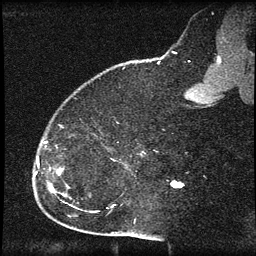
Breast MRI (dynamic contrast-enhanced), one sagittal slice. Position 17 of 60 along the scan axis. Dynamic contrast-enhanced series, image 2 of 3 at this slice position (ordered by acquisition). 1.5 T. TE 4.2 ms, TR 8.2 ms. 256 × 256 image matrix, field of view 180 × 180 mm. Patient: female, 32 years.
Annotated regions visible in this slice (semi-automatic segmentation, software-assisted and operator-edited):
- analysis volume of interest (the breast-tissue region the enhancement analysis was run in; not a lesion): box from (x=32, y=138) to (x=64, y=184) px
- tumour enhancement mask (voxels above the 70 % enhancement threshold inside the analysis volume of interest): (x=37, y=158)–(x=39, y=160)